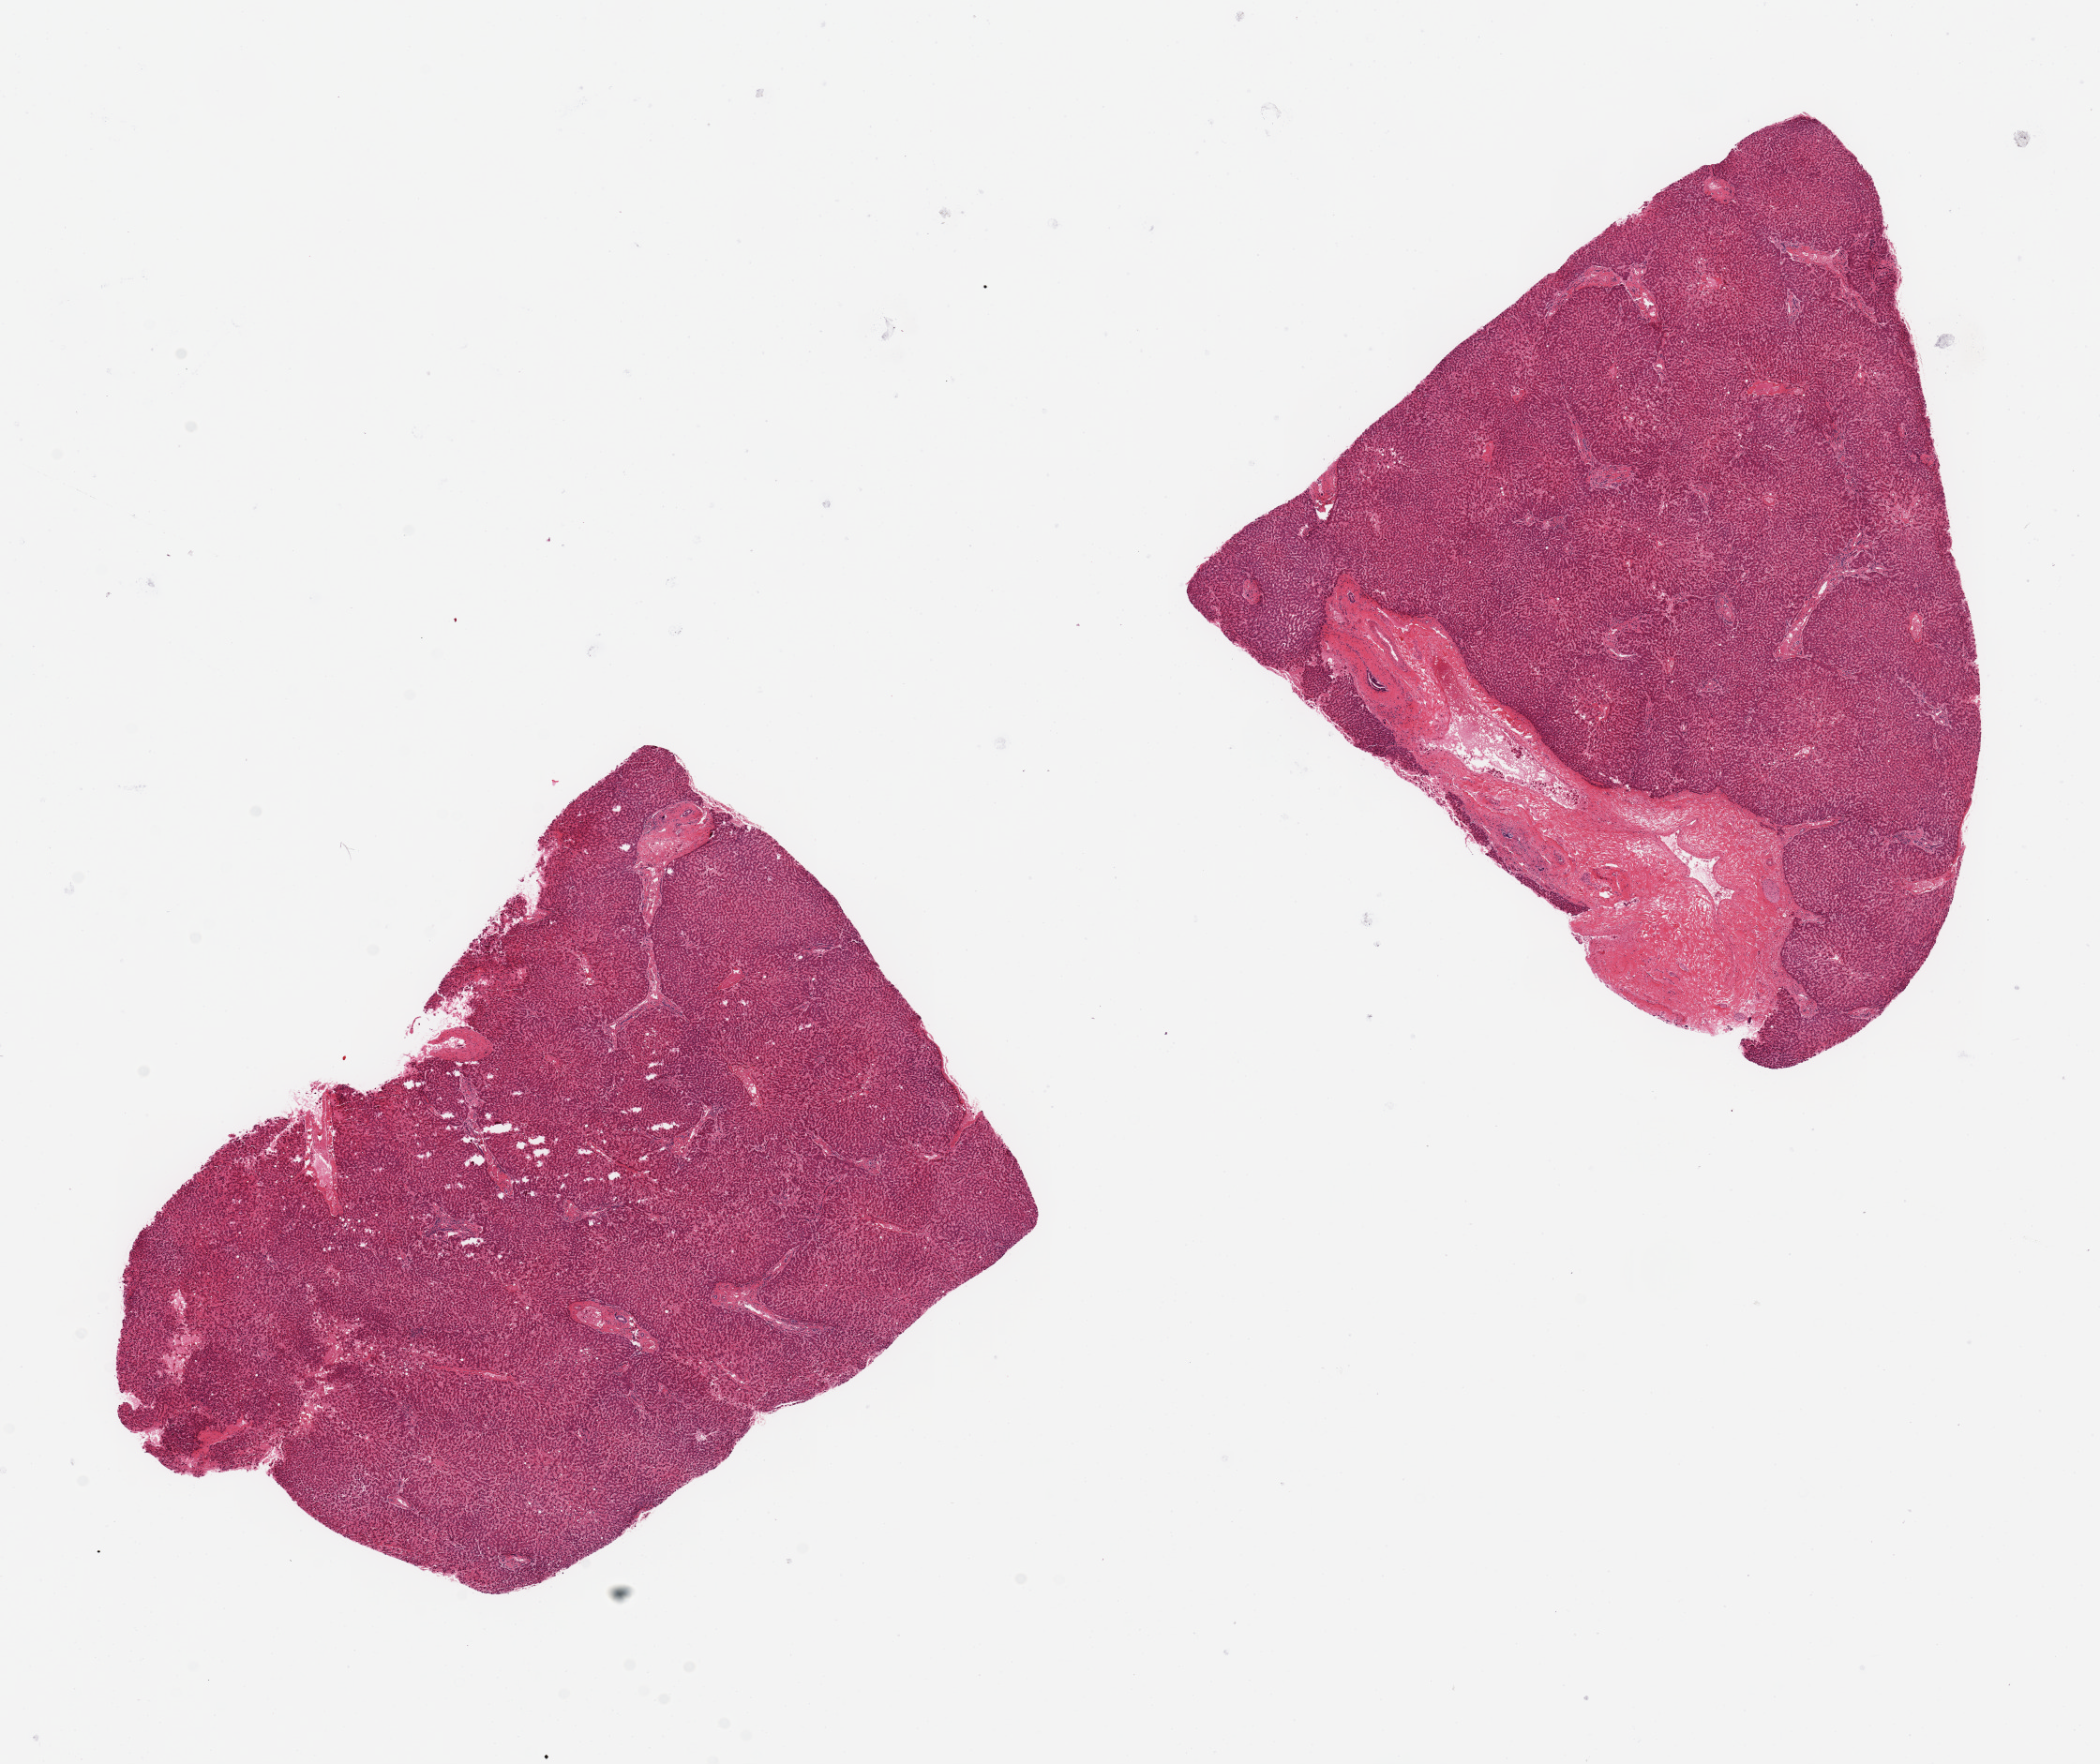
Whole-slide image, H&E stain, brightfield — whole scanned area (about 17.7 x 14.9 mm, from a 20x scan) shown as a low-resolution overview. PAXgene-fixed paraffin-embedded (PFPE) section. Target tissue: liver. Donor tissue sample. Male donor.
Pathologist's review note for this sample: 2 pieces,~7.5x5.5mm;6.5 mm sq. slightly congested.